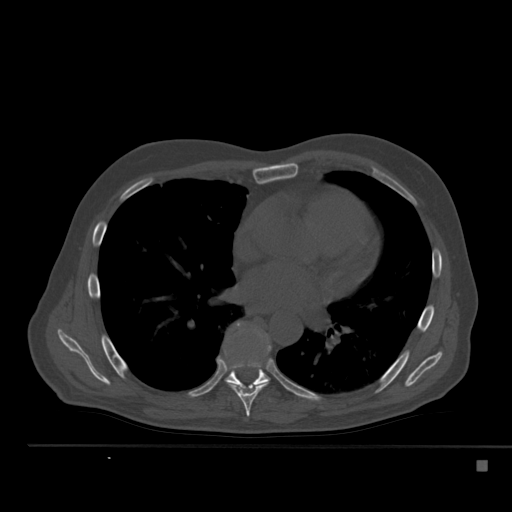
CT including the spine, one axial slice; position 319 of 517 along the scan axis; reconstruction kernel Br40s; 120 kVp; bone window (W 1800 / L 400 HU); 1.5 mm slice thickness; 512 × 512 image matrix, field of view 408 × 408 mm. Patient: male, 70 years. From the clinical record (not read from this slice): primary cancer: renal.
Outlined on this slice (semi-automatically segmented with operator editing):
- T7 vertebra: bounding box (x1, y1, x2, y2) in pixels: (226, 350, 270, 417)
- T8 vertebra: (225, 322, 271, 392)